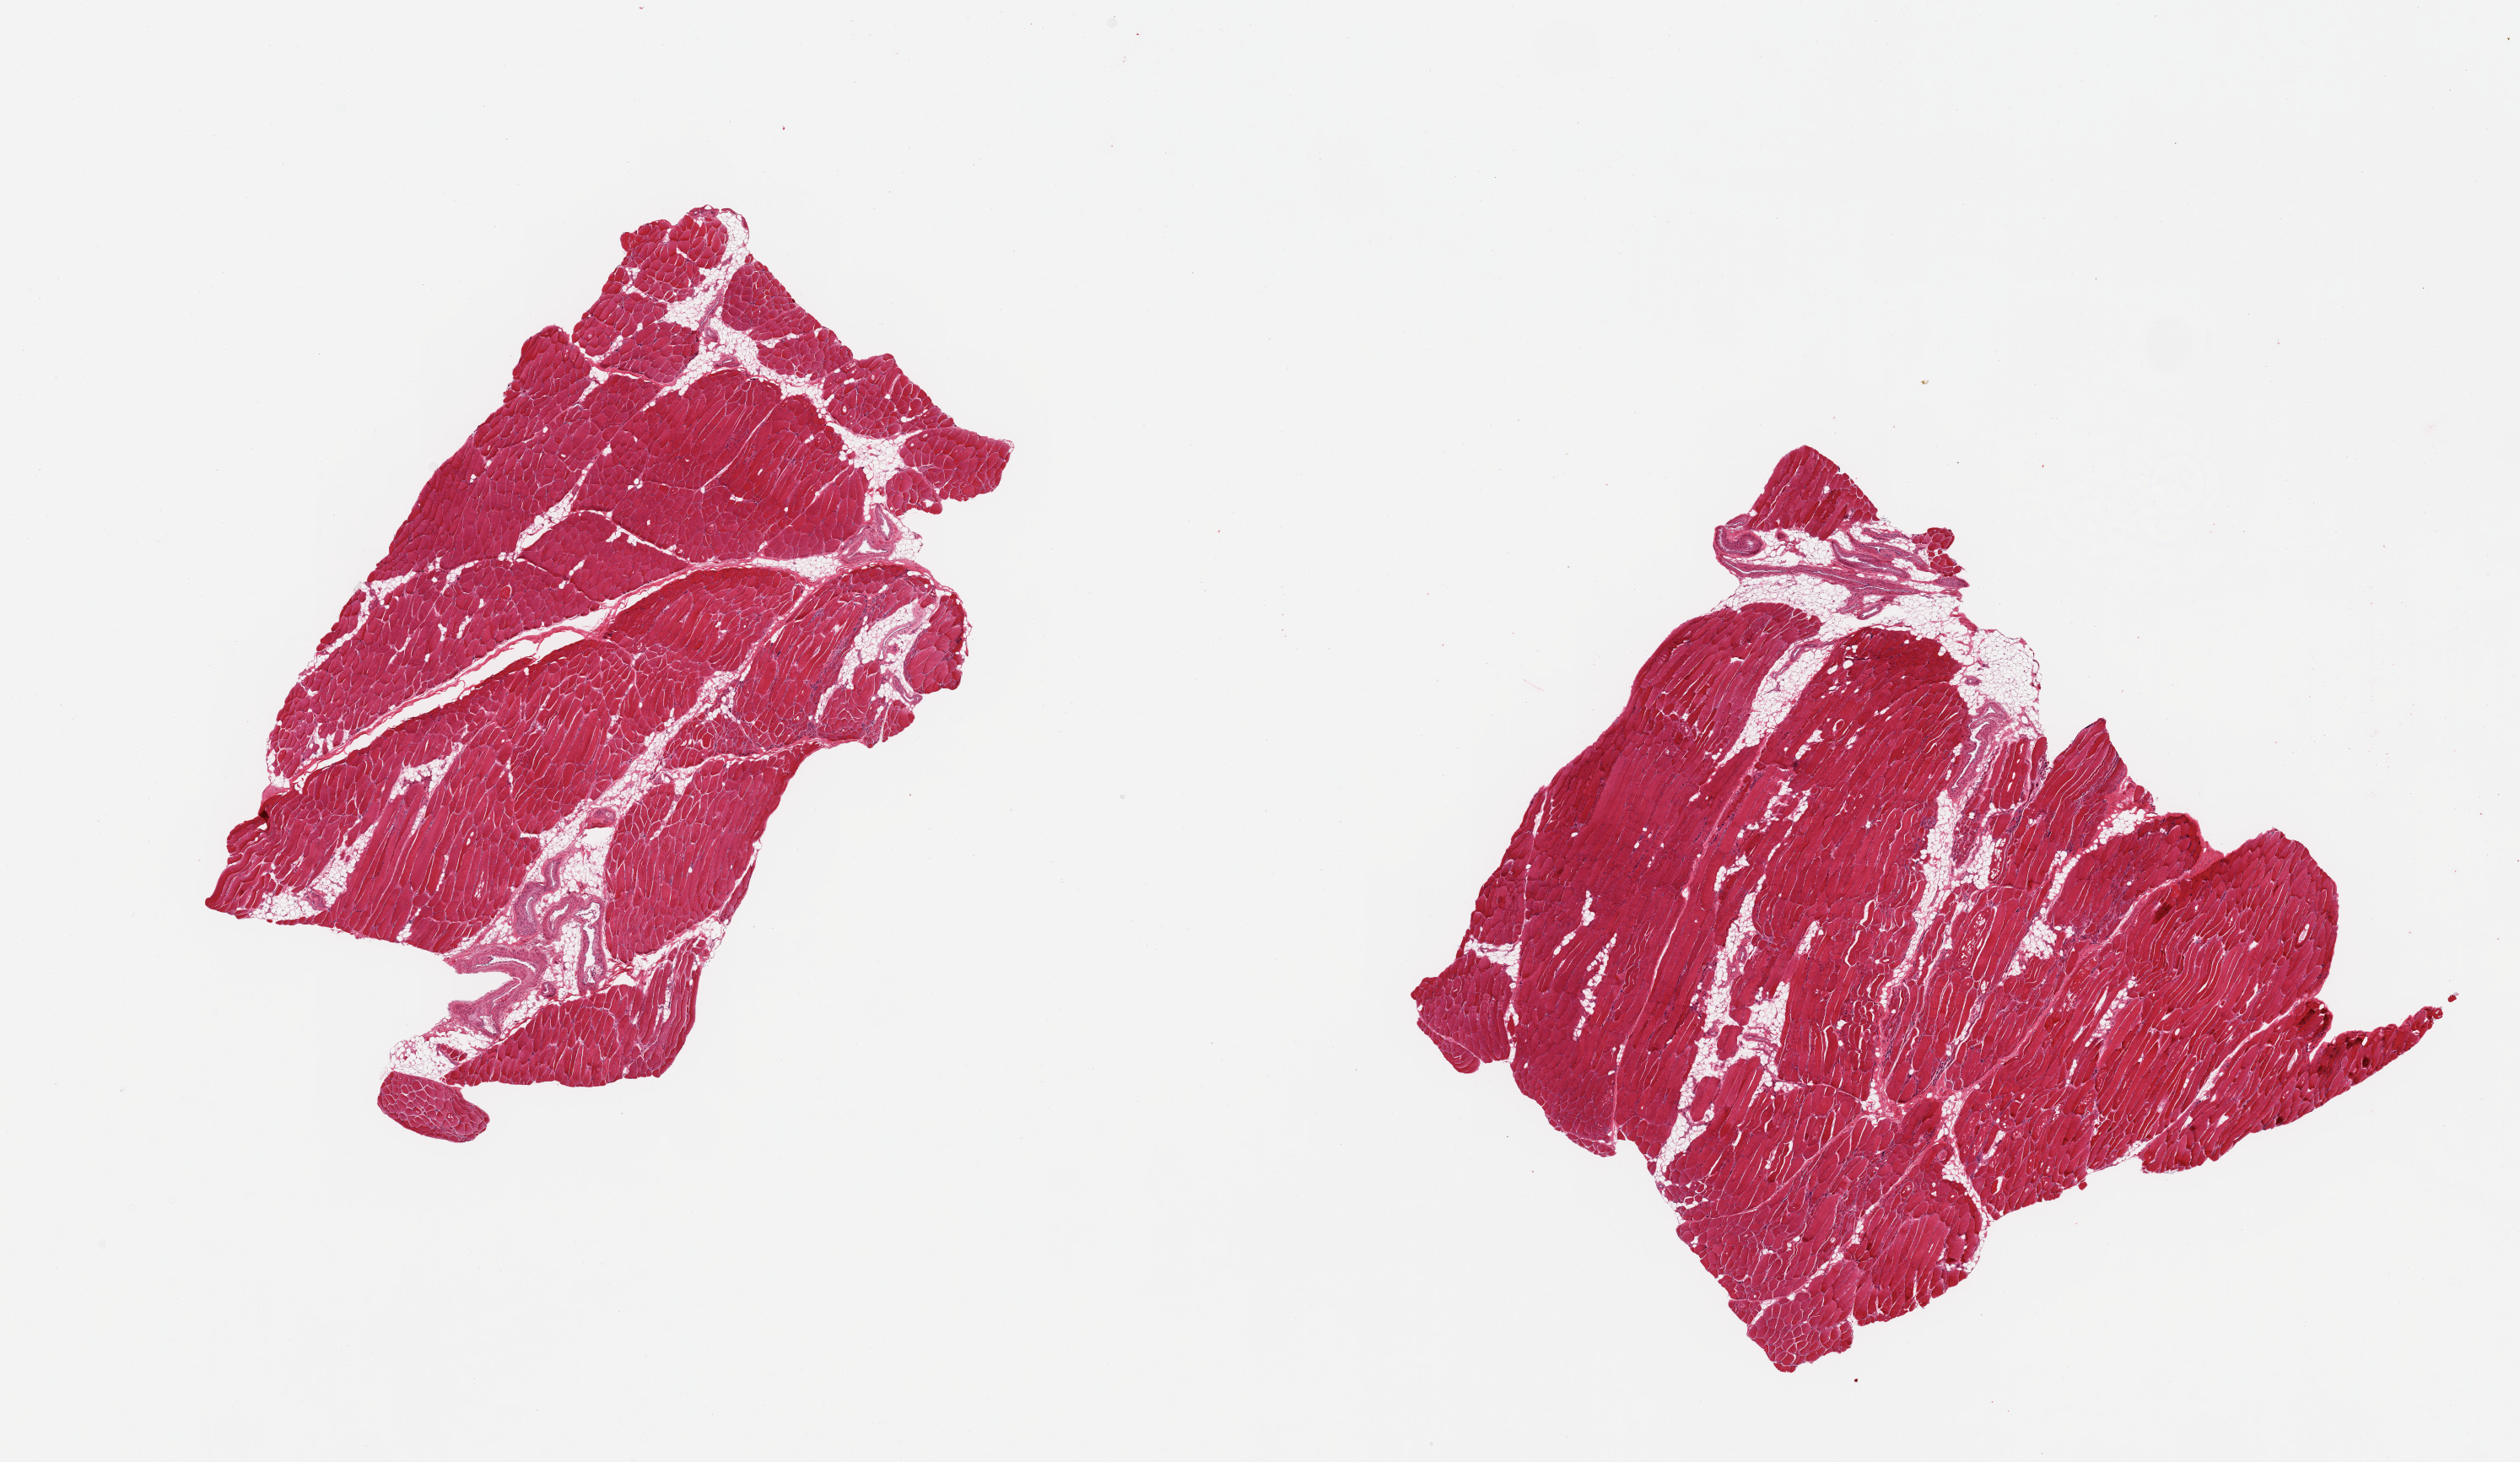
H&E whole-slide image, brightfield — low-resolution overview of the scanned area, about 23.6 x 13.7 mm, PAXgene-fixed paraffin-embedded (PFPE) section, sampled site (target tissue): skeletal muscle, donor tissue sample. Donor: male.
• review note (as recorded): 2 pieces; ~15% internal fat, patchy atrophy